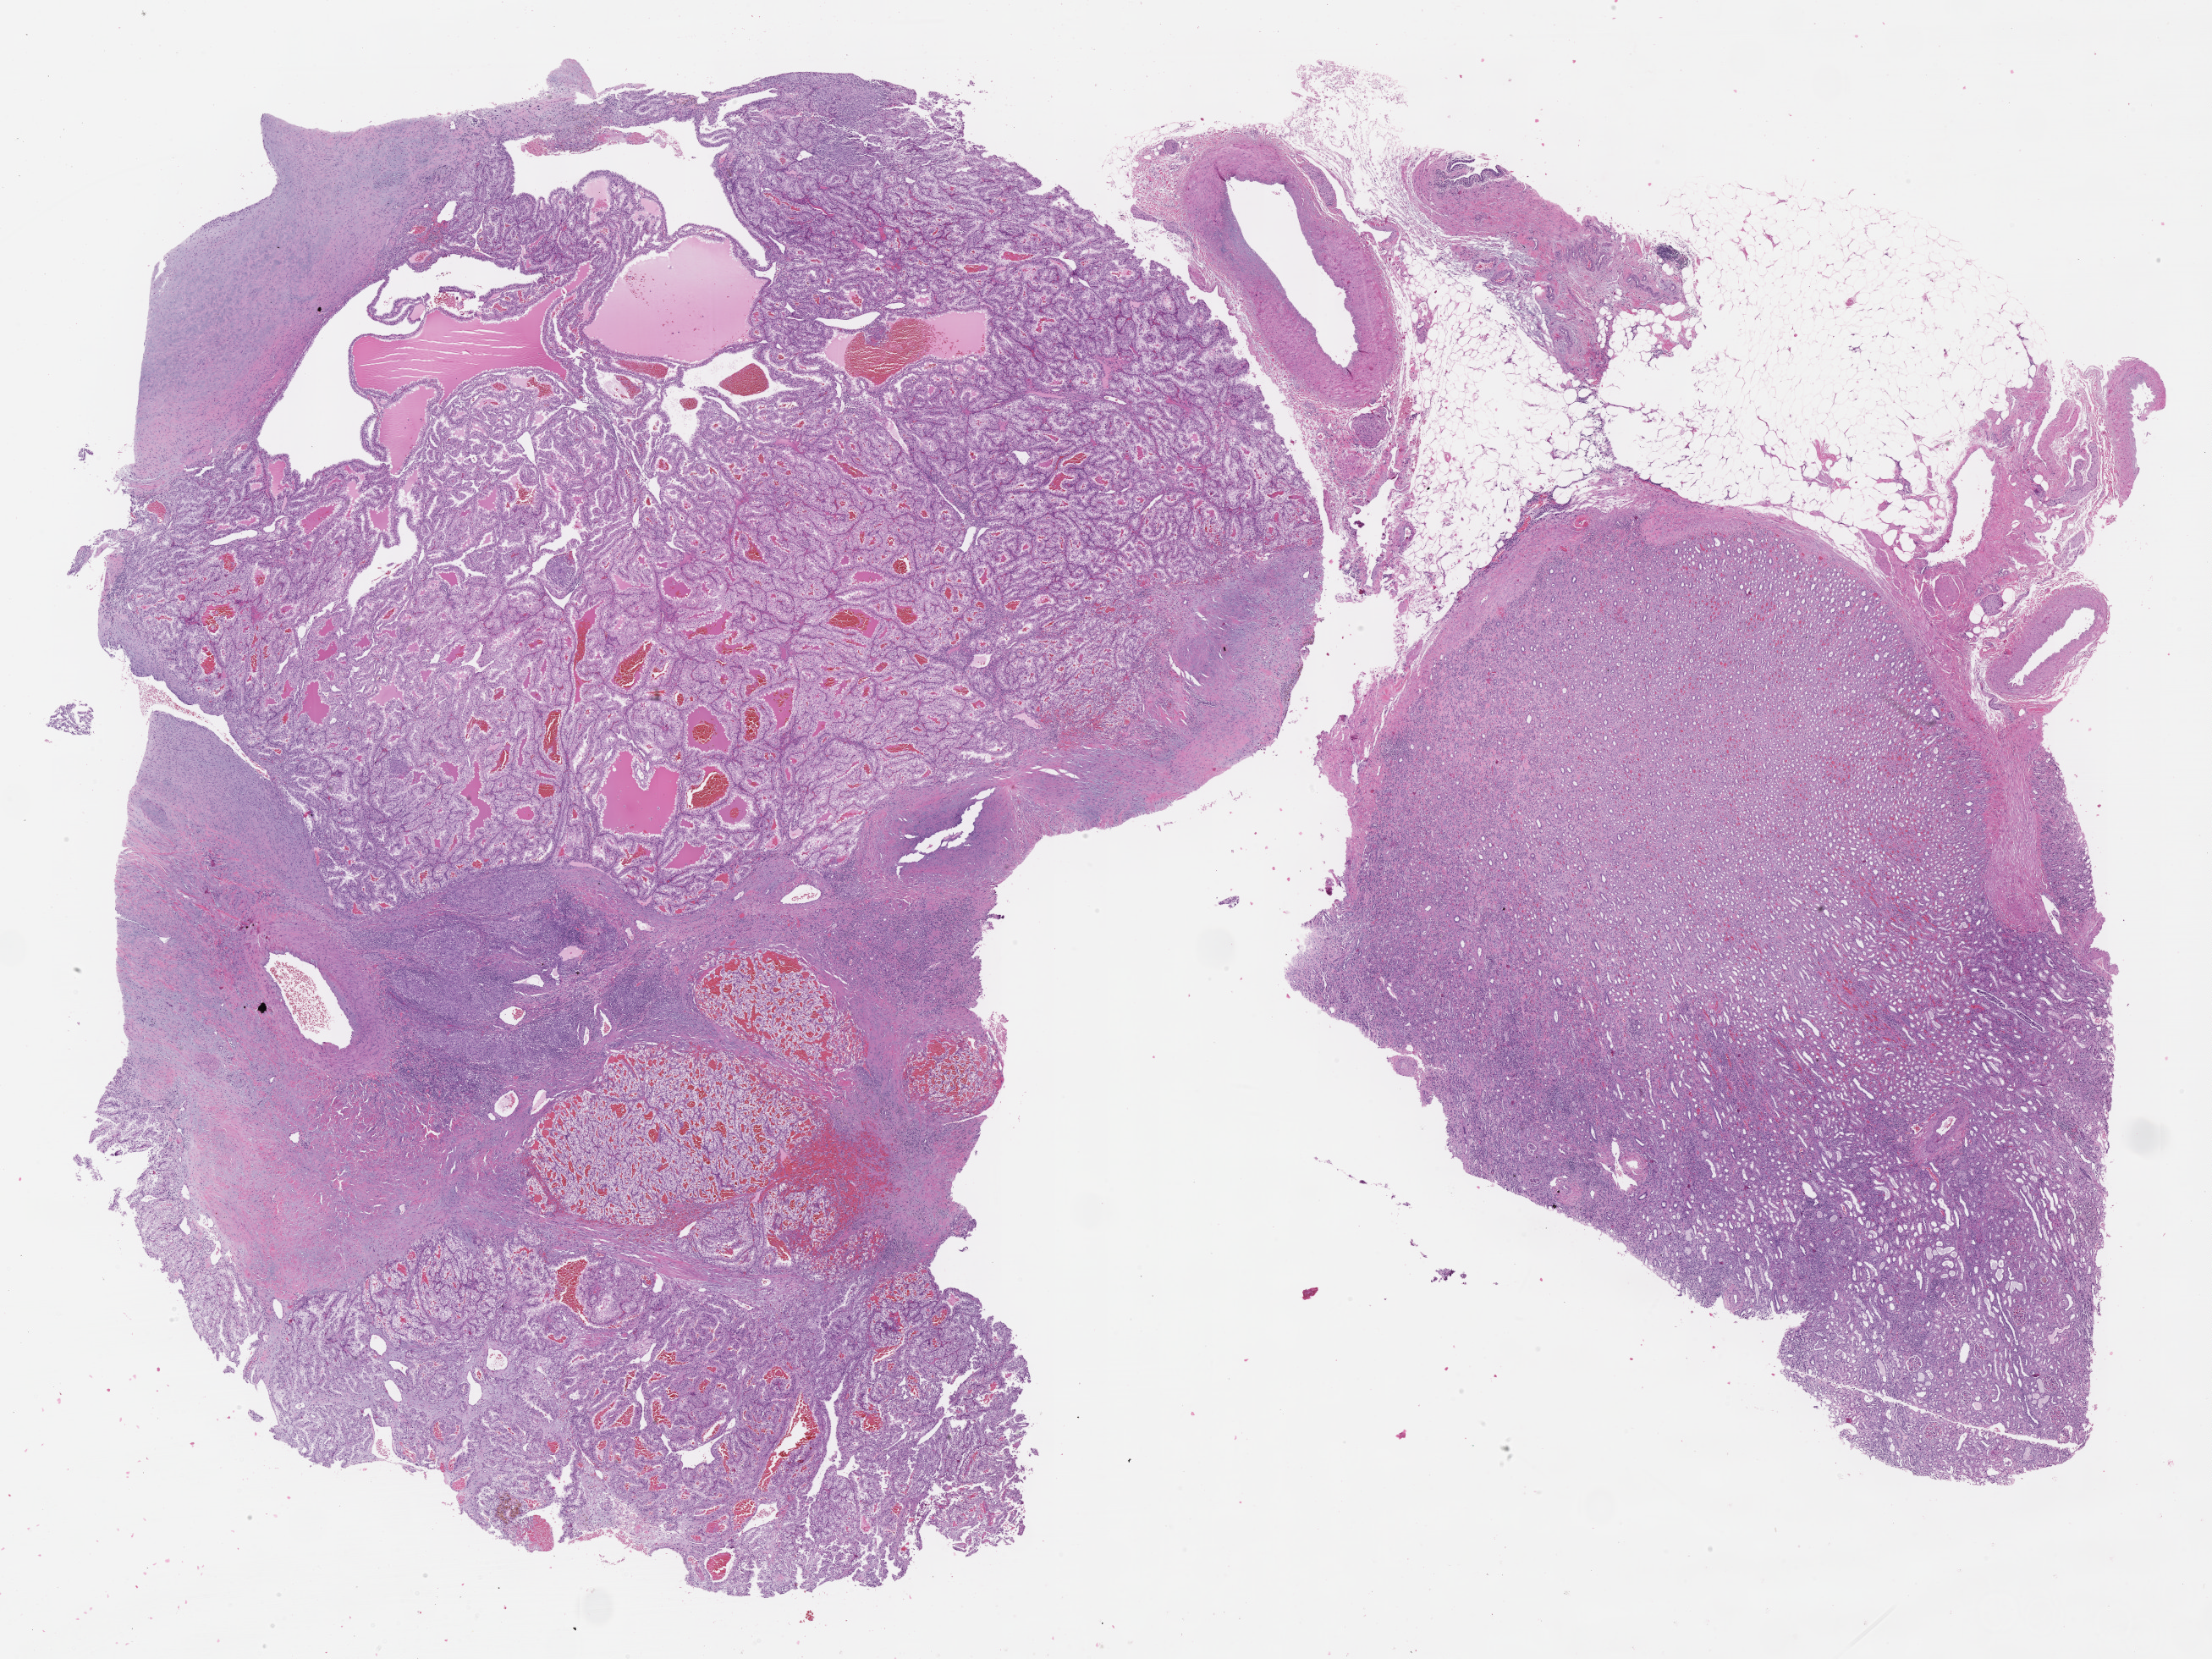
Digitized Hematoxylin and eosin (H&E) stained tissue section (whole slide), shown as a low-resolution overview of the whole scanned area (about 21.1 x 15.8 mm, from a 40x scan), formalin-fixed paraffin-embedded (FFPE) diagnostic section, sample: primary tumour, kidney. Patient: male, age at initial diagnosis 54 years. Histologic grade: G3 (poorly differentiated).
• AJCC pathologic stage: I (7th edition)
• diagnosis: Clear cell adenocarcinoma, NOS